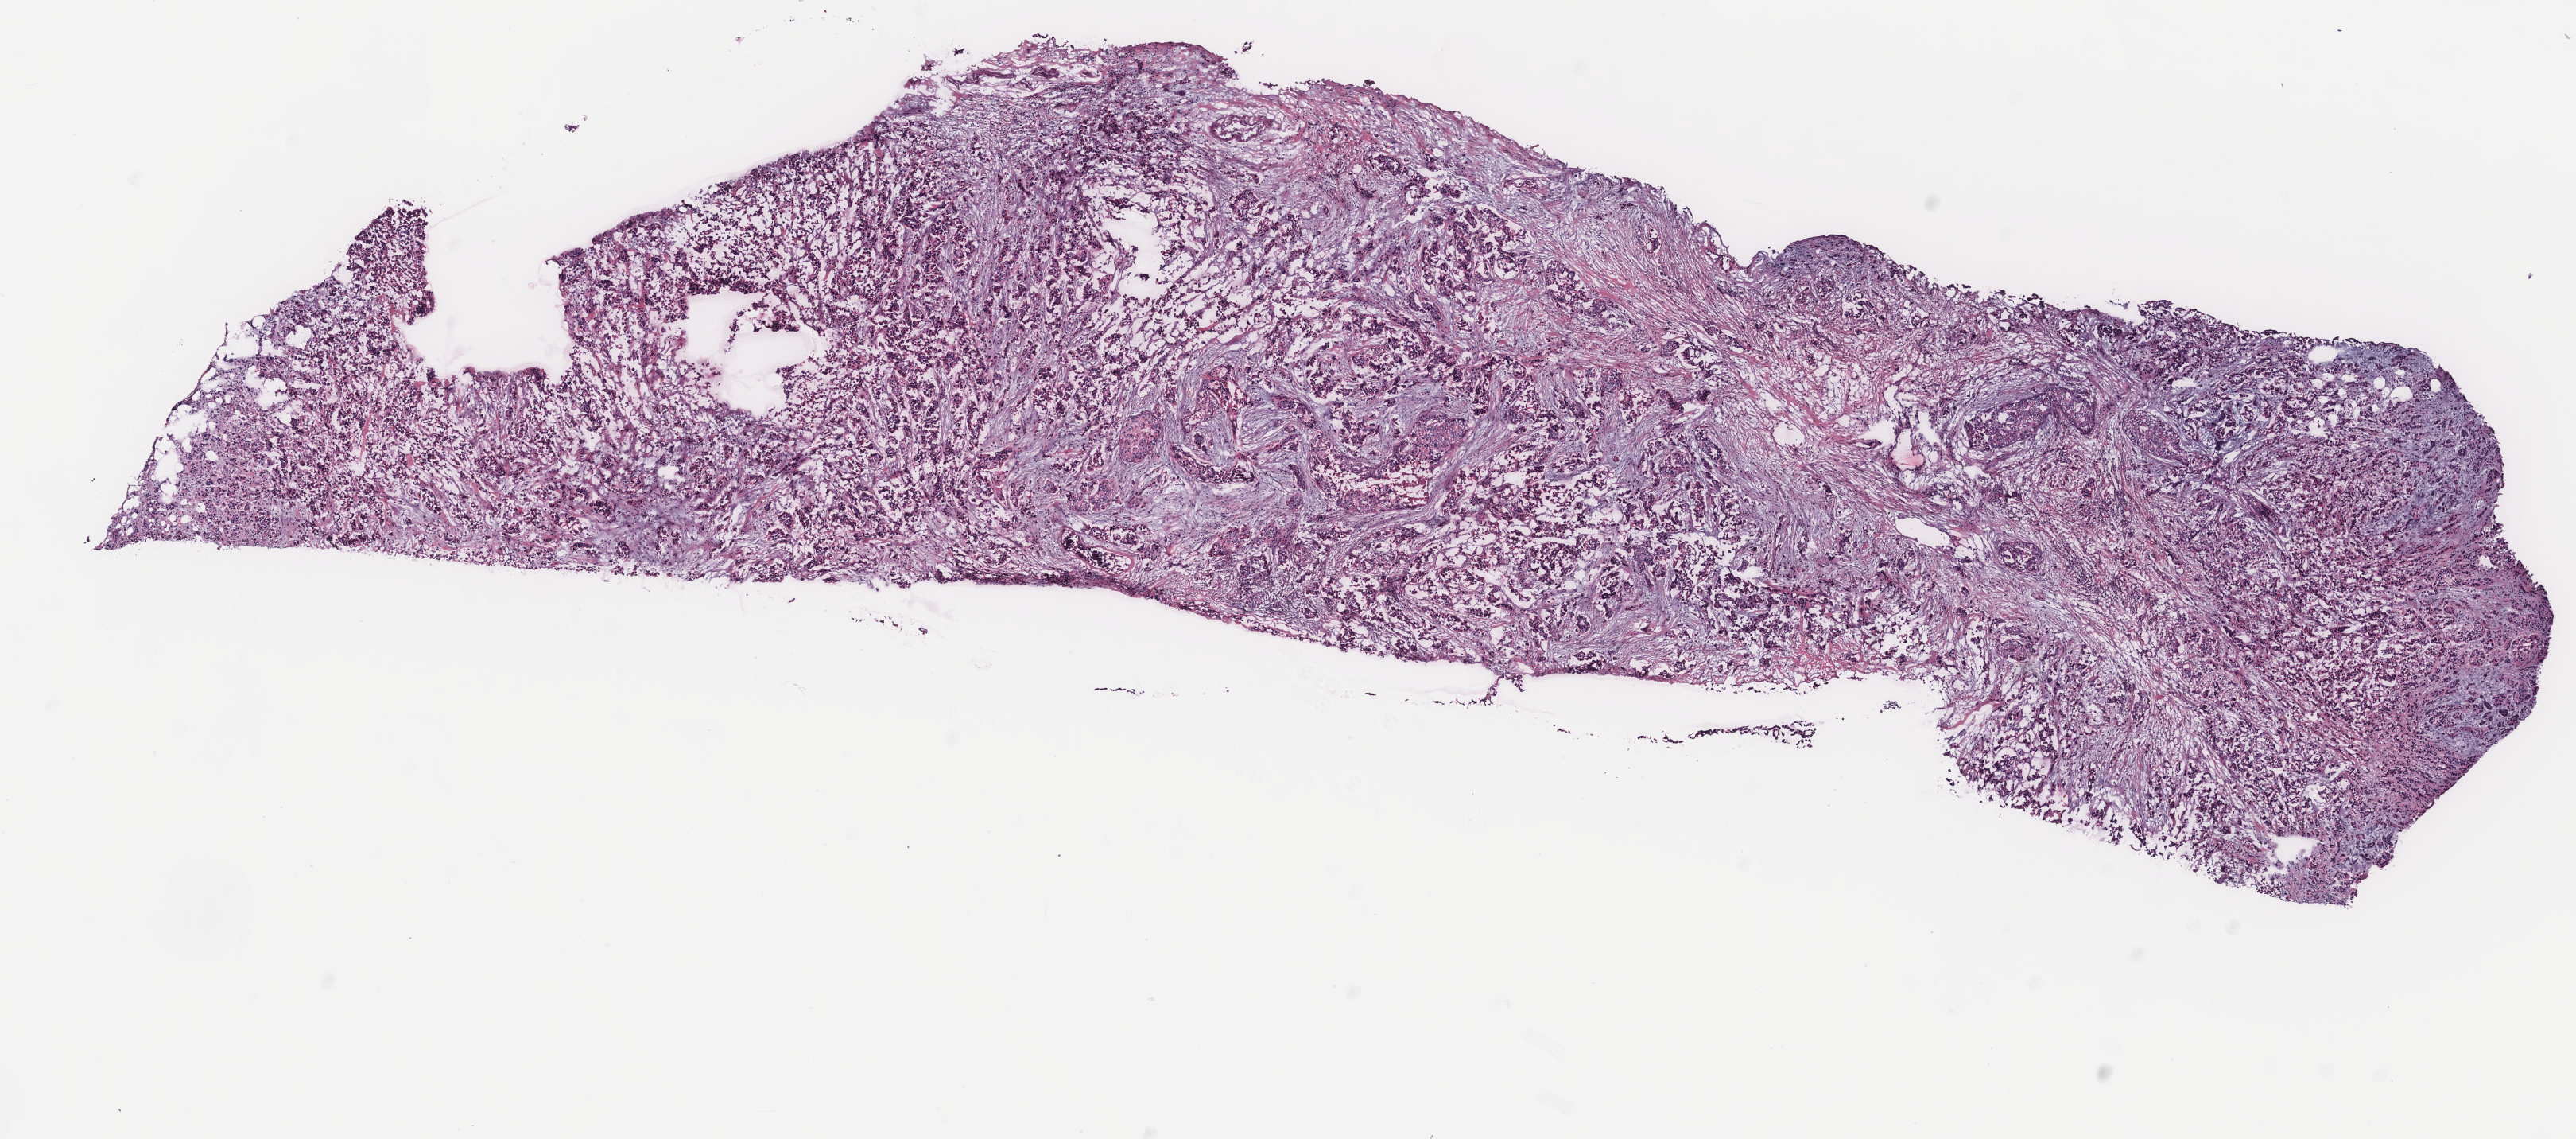
Whole-slide histology image, H&E-stained — a low-resolution overview of the entire scanned area, about 13.0 x 5.7 mm (from a 40x scan); tumour tissue sample, breast. 58-year-old female patient.
AJCC pathologic stage: IIA. Diagnosis: Infiltrating duct carcinoma, NOS.